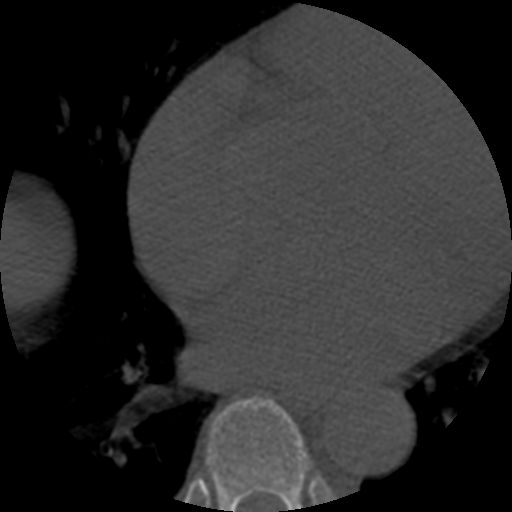
CT including the spine, one axial slice; position 337 of 508 along the scan axis; reconstruction kernel STANDARD; 120 kVp; bone window (W 1800 / L 400 HU); 512 × 512 image matrix, field of view 160 × 160 mm. Patient age 57 years. Case-level facts recorded for this patient, not image findings: primary cancer: prostate.
Structures marked on this image (semi-automatically segmented with operator editing):
- T7 vertebra: bounding box <206,396,310,512> (left, top, right, bottom; pixels)